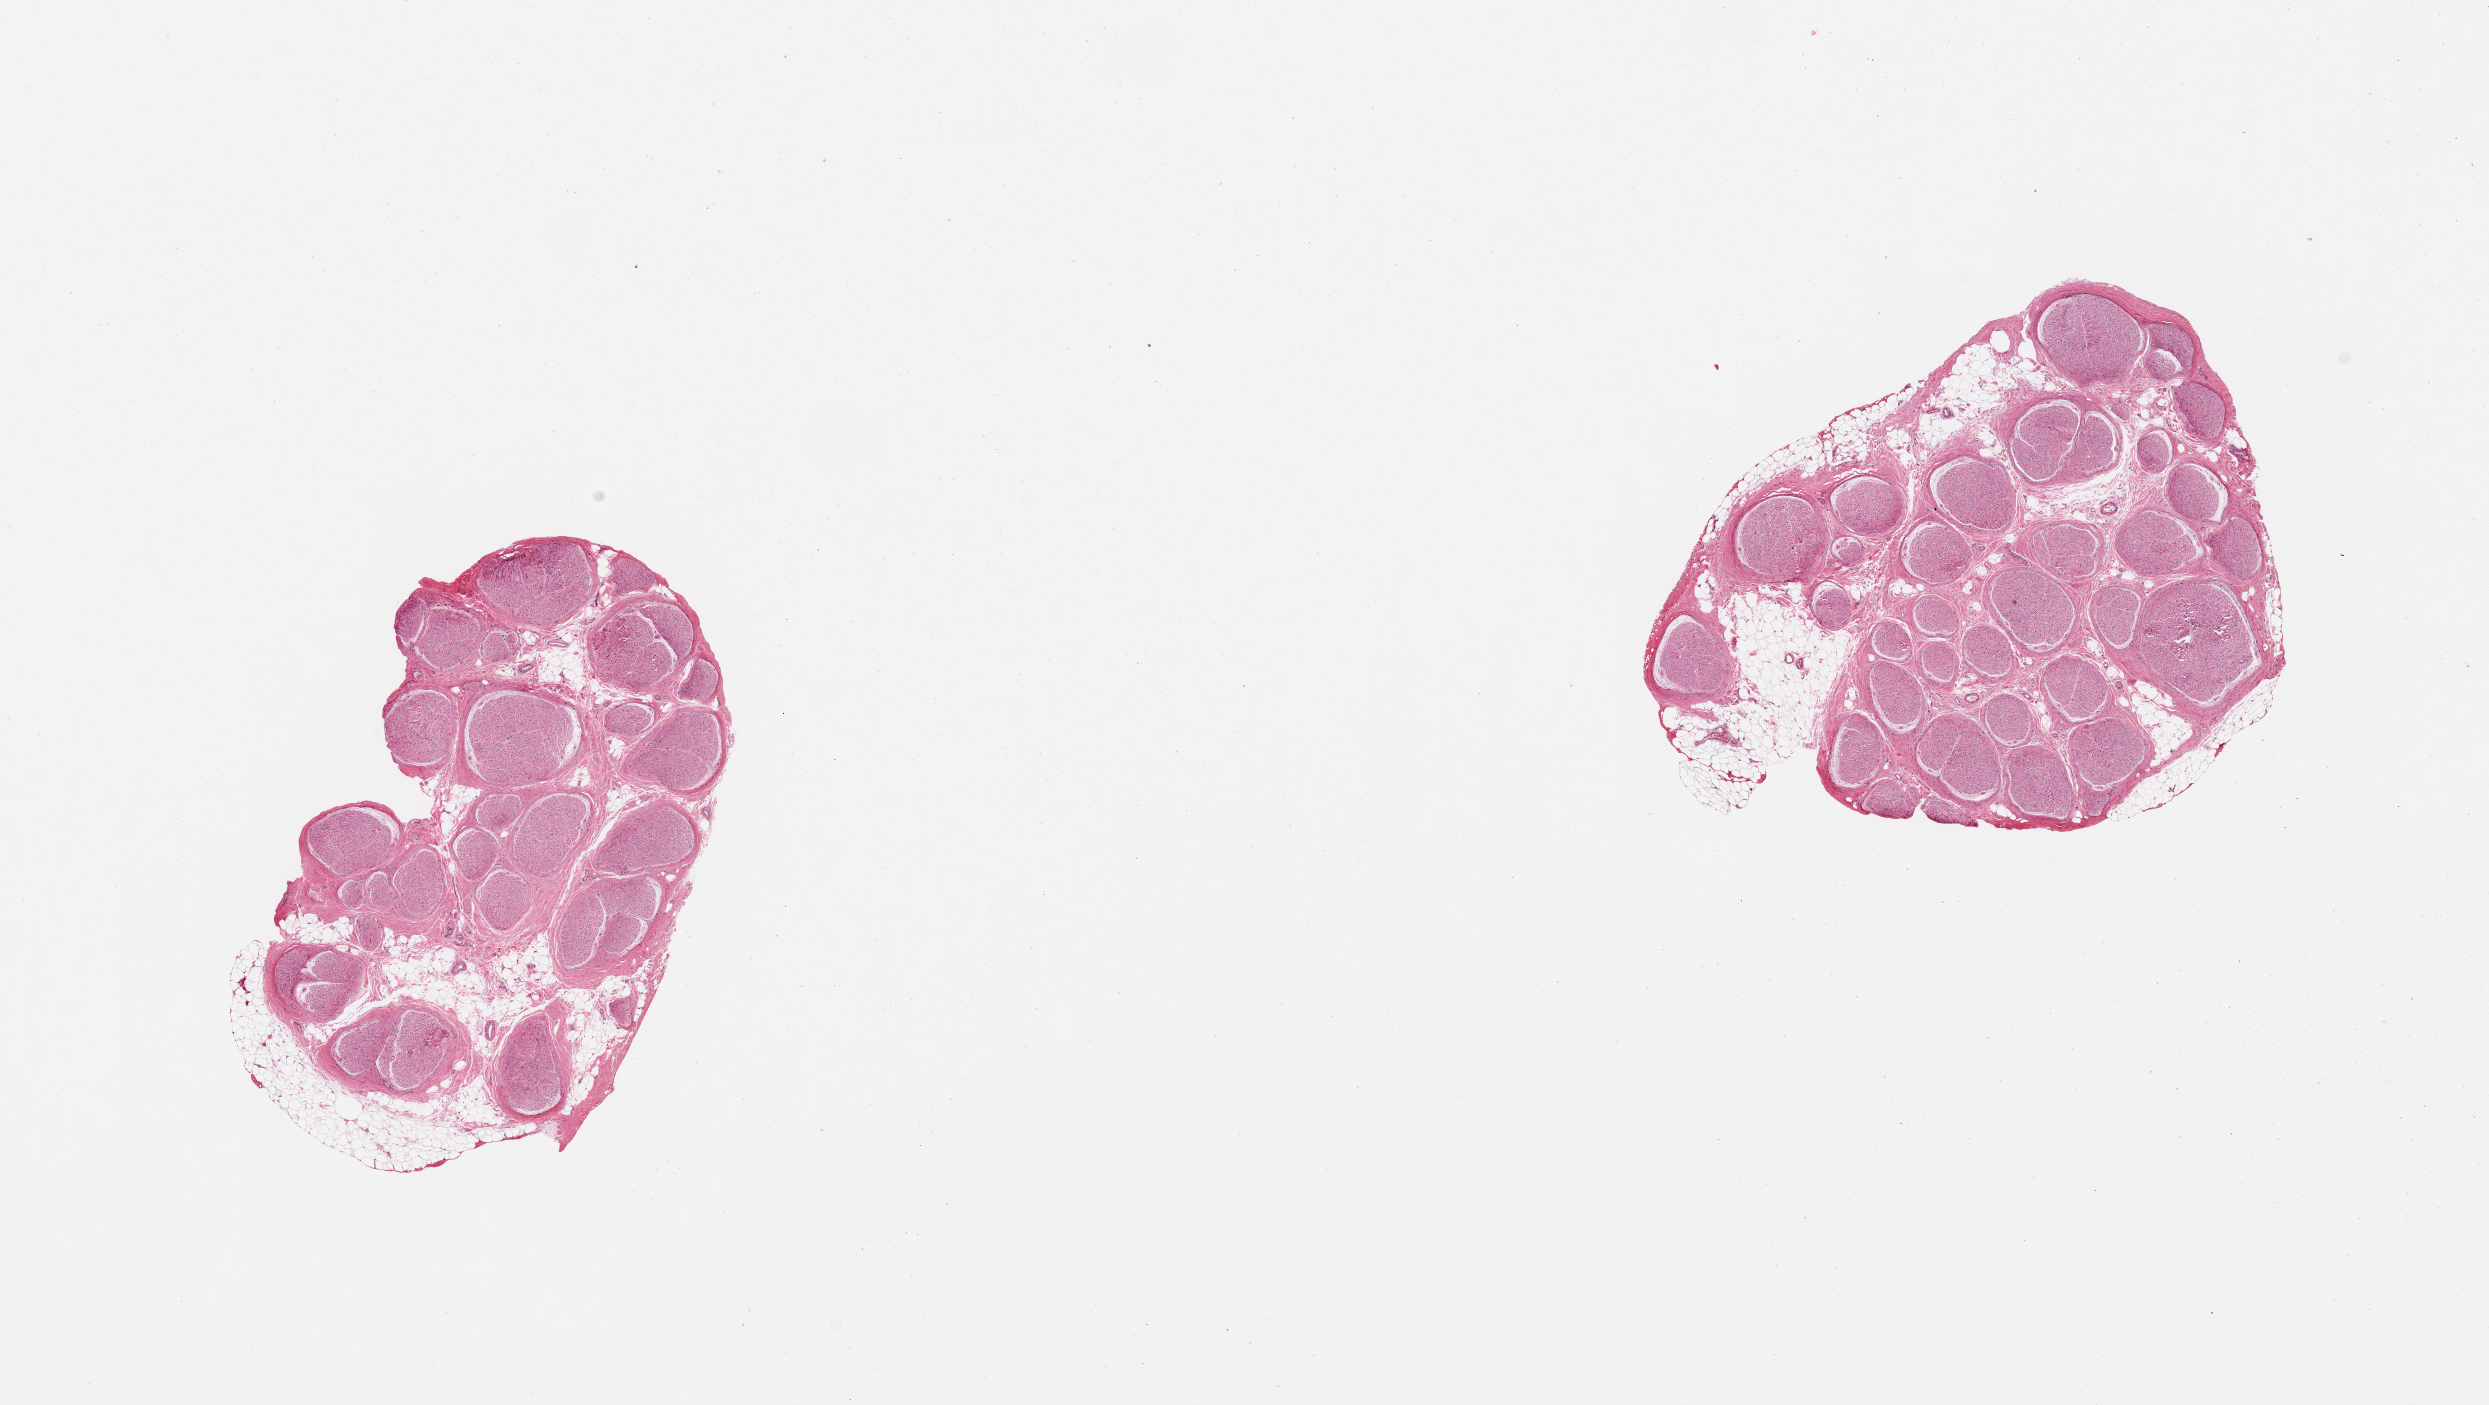
Digitized haematoxylin and eosin-stained section — whole scanned area (about 19.7 x 11.1 mm) shown as a low-resolution overview; PAXgene-fixed, paraffin-embedded tissue; target tissue: tibial nerve; tissue donor sample. Donor sex: female.
Review note (as recorded): 2 pieces trace nubbin of adherent fat up to ~0.5mm.